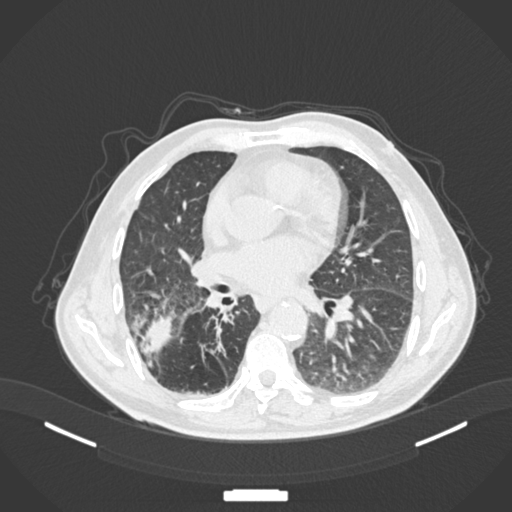
Chest CT, one axial slice. Position 74 of 201 along the scan axis. Lung window (W 1500 / L -600 HU). 1 mm slice thickness. 512 × 512 image matrix. Patient: male, 72 years. From the clinical record (not read from this slice): clinical TNM (as recorded): T3 N2 M0.
Outlined on this slice (rectangle marked by the reading radiologist):
- lung tumour (recorded histology: adenocarcinoma): bounding box <139,314,175,353> (left, top, right, bottom; pixels)